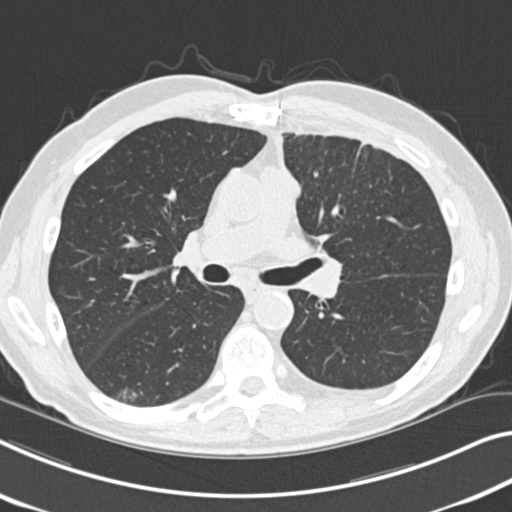
Chest CT (low-dose screening protocol), one axial image, first (baseline) screen, lung window (W 1500 / L -600 HU), 120 kVp, slice 97 of 212 in the series. Male participant, aged 68 years at enrolment. Current smoker at enrolment.
- Expert reader's lesion annotation, bounding box <99,380,149,414> (left, top, right, bottom; pixels).
- The exam's reader record, not a measurement of the box and not confirmed to be the same lesion: non-calcified nodule or mass ≥4 mm, right lower lobe, 14 × 10 mm, poorly defined margins, ground glass attenuation.
- Participant outcome: lung cancer diagnosed 1018 days after this screen (after the third annual screen) — non-small cell carcinoma, right lower lobe, poorly differentiated (G3), stage IA (AJCC 6th edition), 23 mm at pathology.